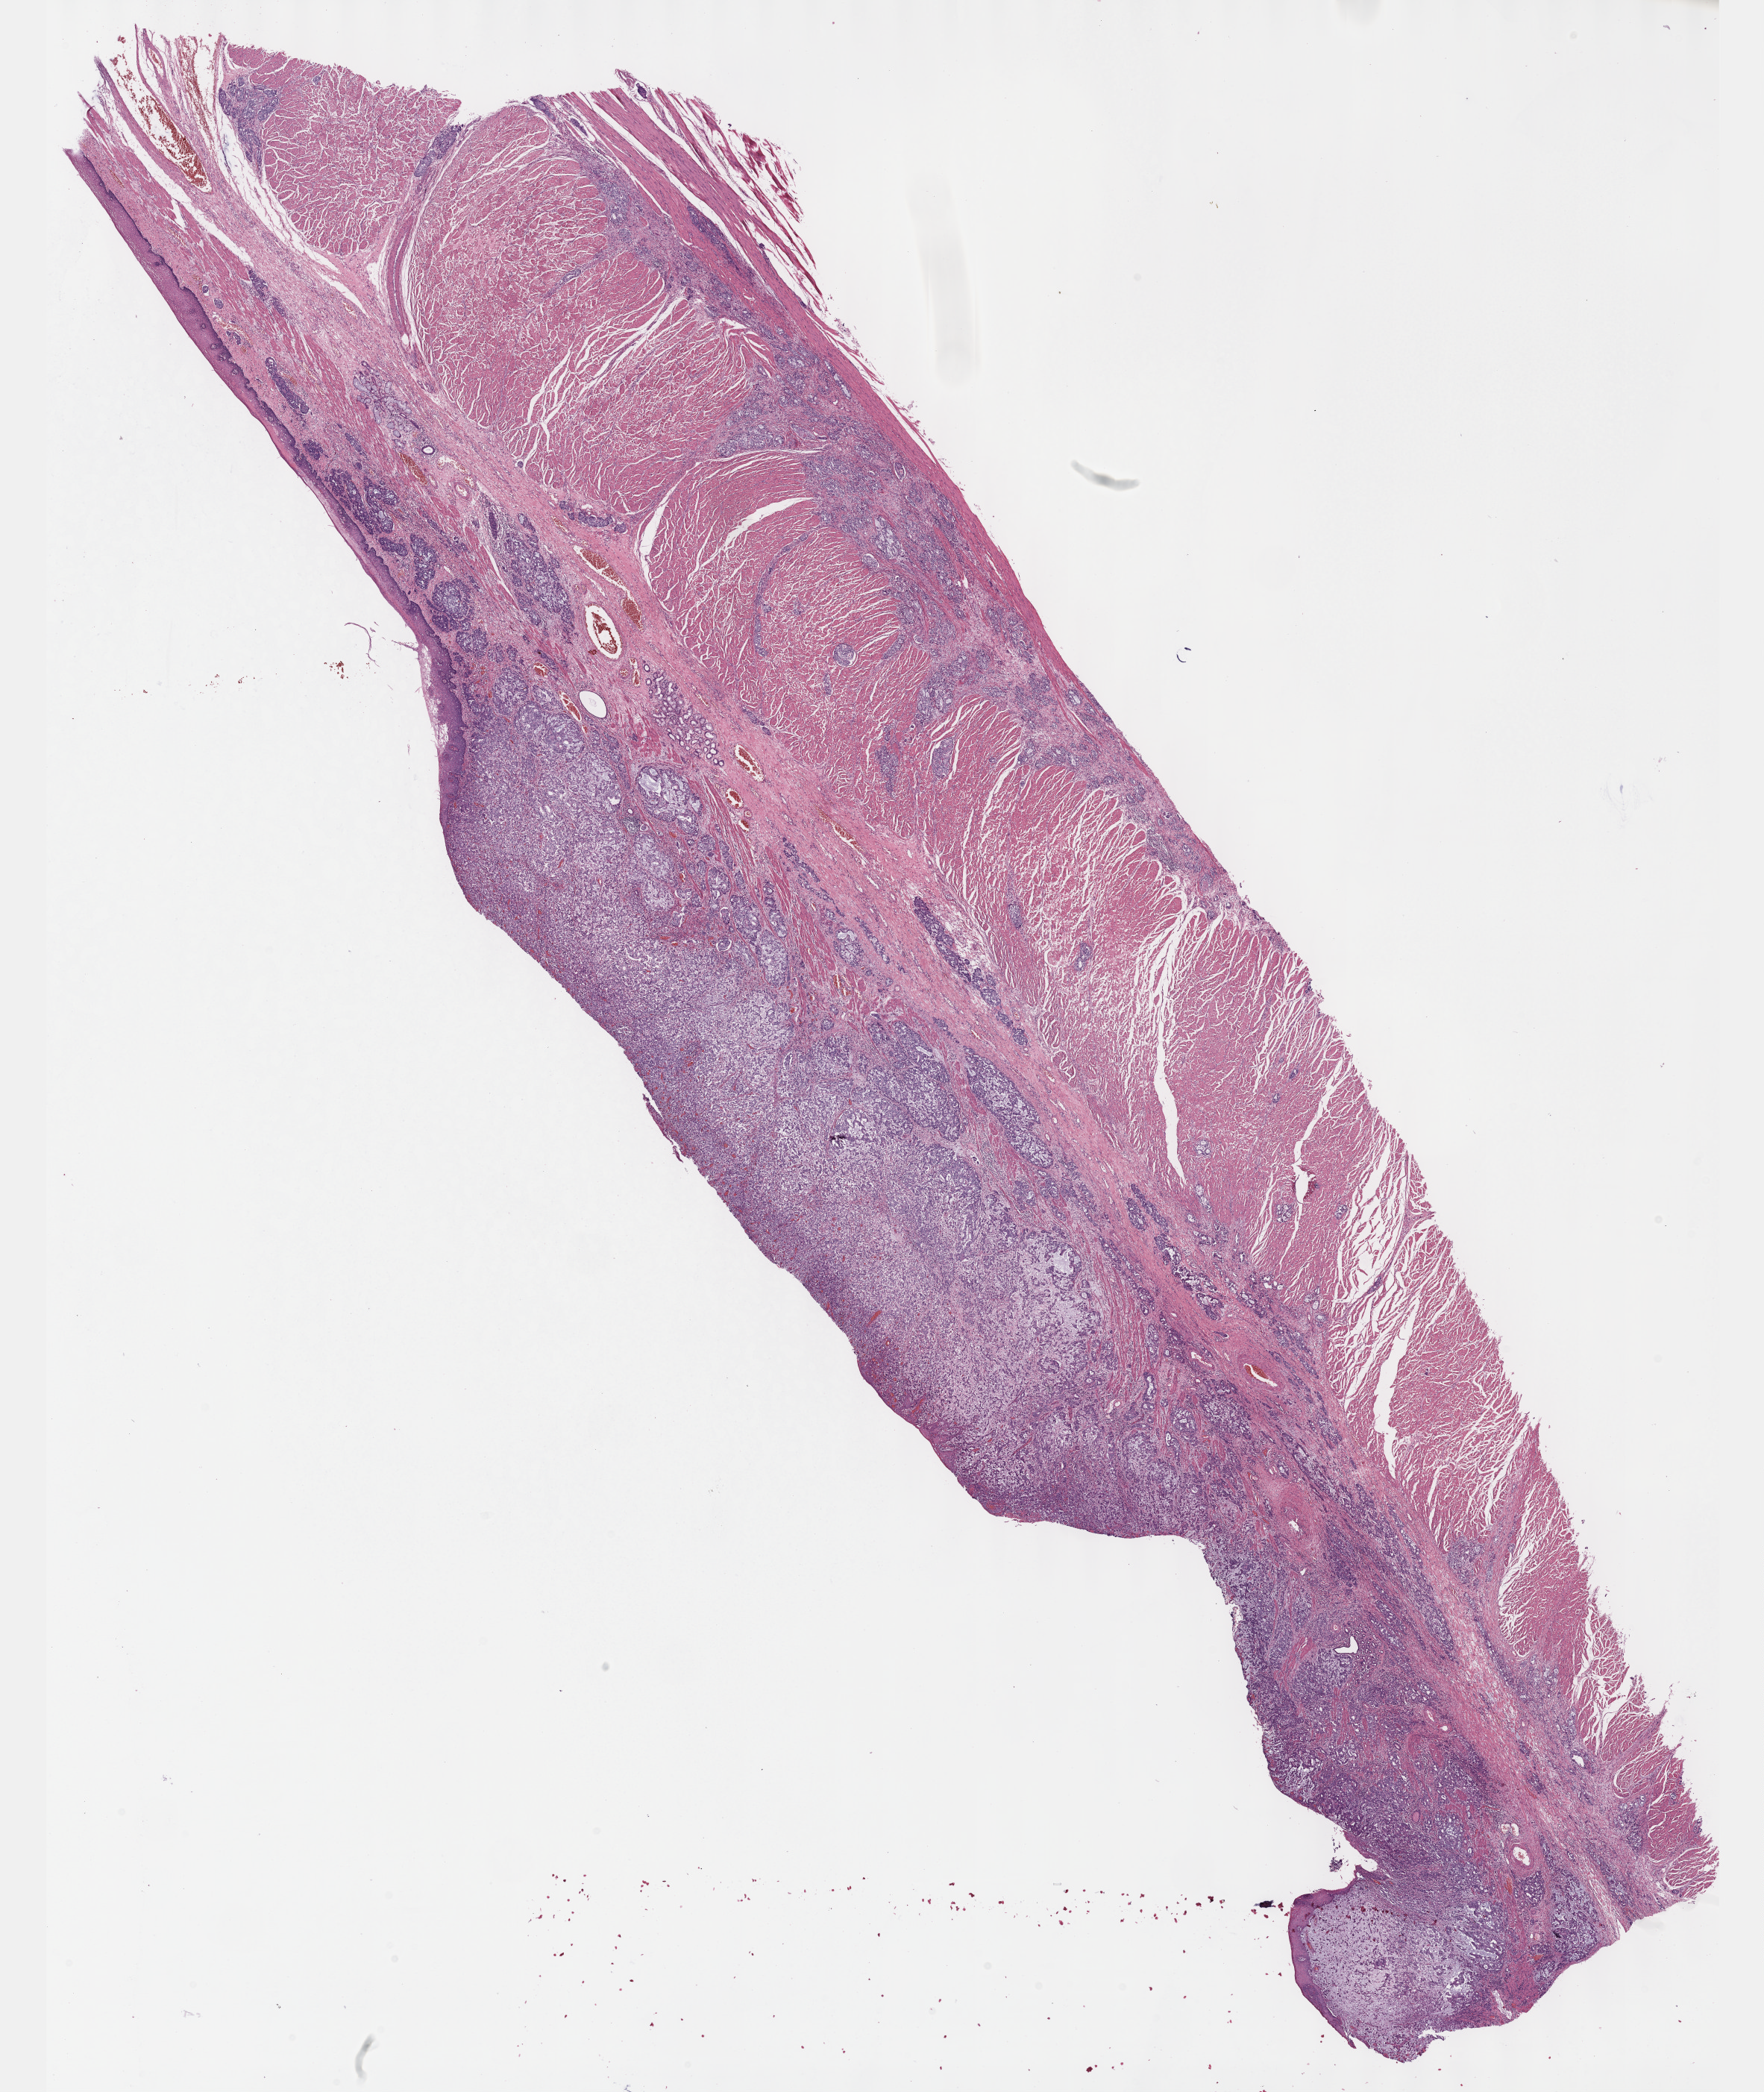
H&E whole-slide image — whole scanned area (about 19.1 x 22.7 mm, from a 40x scan) shown as a low-resolution overview; formalin-fixed paraffin-embedded (FFPE) diagnostic section; sample: primary tumour, stomach. Male, age 61 years at initial diagnosis. Histologic grade: G3 (poorly differentiated).
• lymph nodes positive (case pathology): 25 of 28 examined
• TNM: T3 N3 M0
• AJCC pathologic stage: IV (6th edition)
• diagnosis: Tubular adenocarcinoma (cardia, NOS)